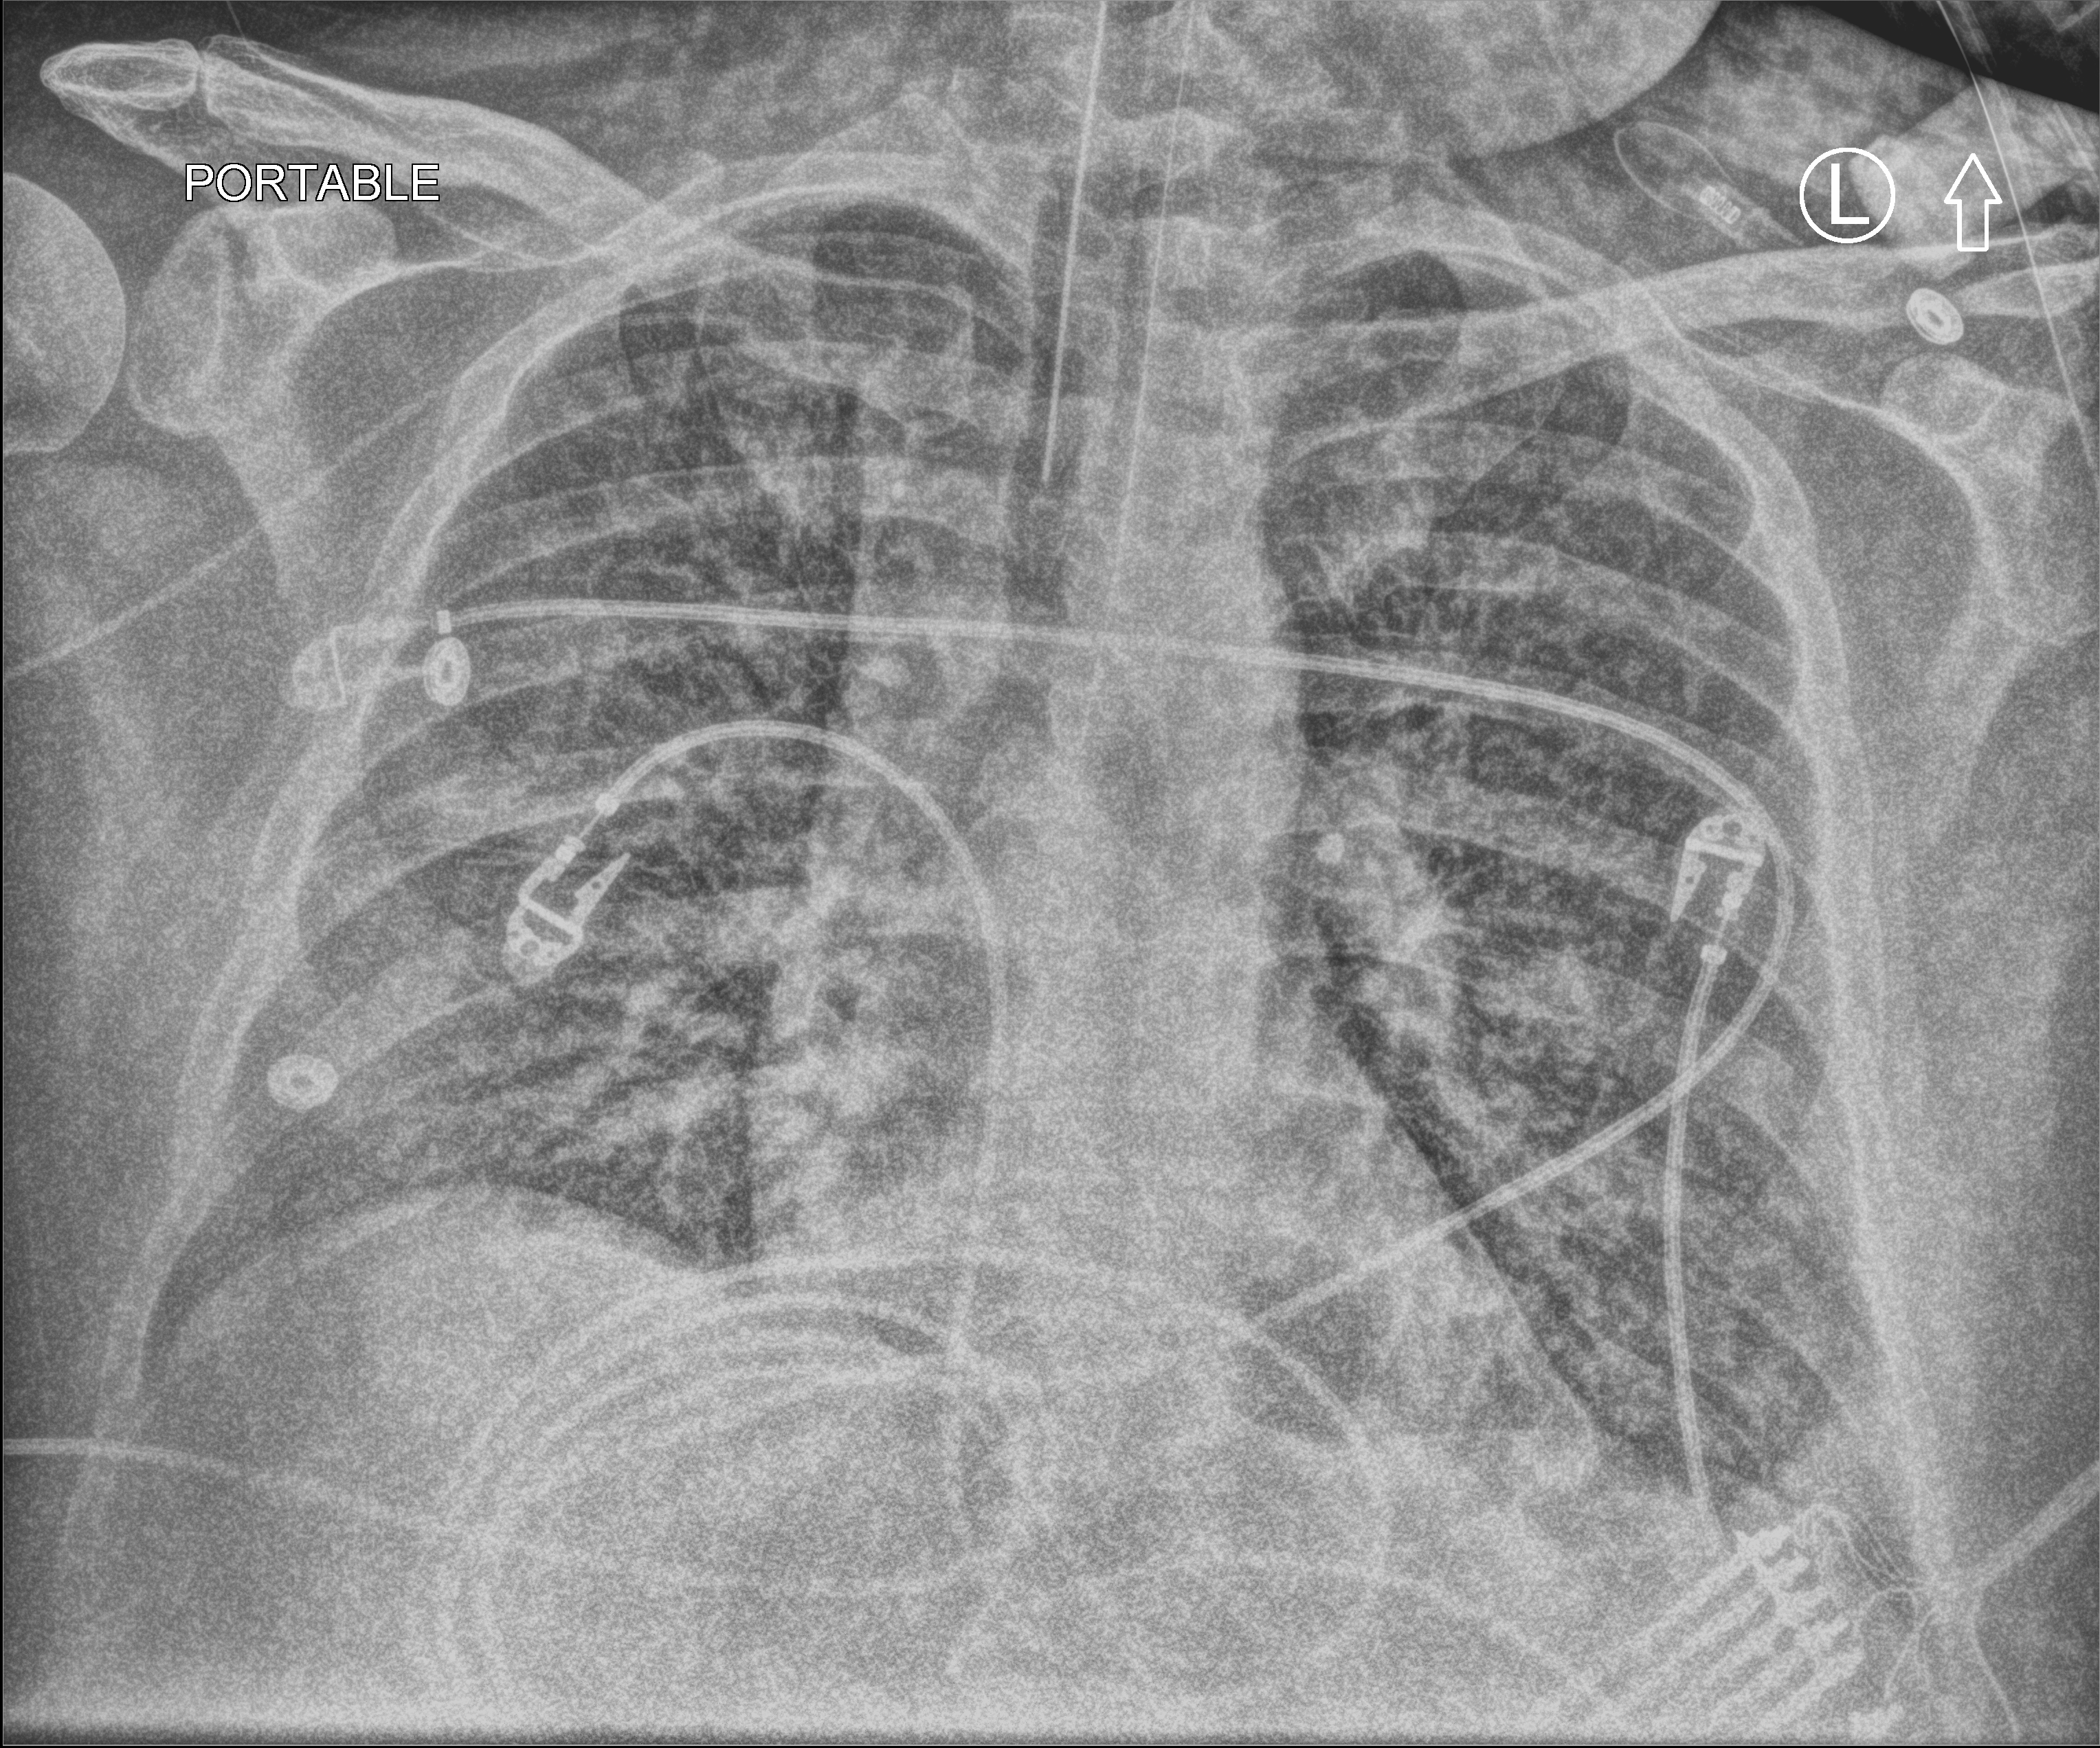
Chest X-ray (portable), anteroposterior (AP) projection. Adult patient hospitalised with COVID-19, age 18–59 years.
From the hospital-stay record, not from the radiograph (when in the stay this image was taken is not recorded):
- hypertension (admission record): yes
- length of hospital stay: 26 days